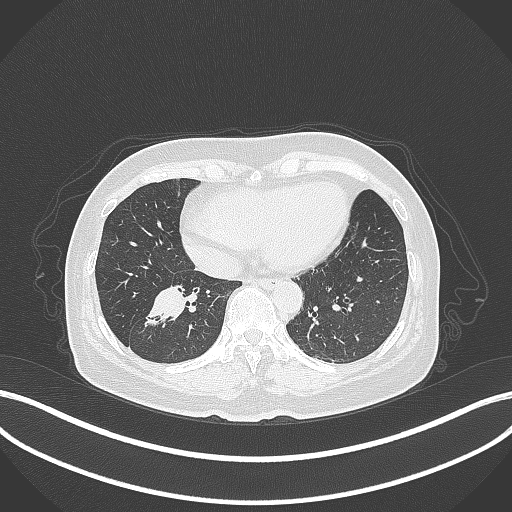
Chest CT, one axial slice. Position 130 of 429 along the scan axis. Reconstruction kernel B70f. Lung window (W 1500 / L -600 HU). 1 mm slice thickness. 512 × 512 image matrix. Female patient, age 67 years. Case-level facts recorded for this patient, not image findings: clinical TNM (as recorded): T1c N1 M0; histopathological grade: G2-3.
Structures marked on this image (rectangle marked by the reading radiologist):
- lung tumour (recorded histology: adenocarcinoma): bounding box [x1, y1, x2, y2] px = [141, 282, 191, 327]